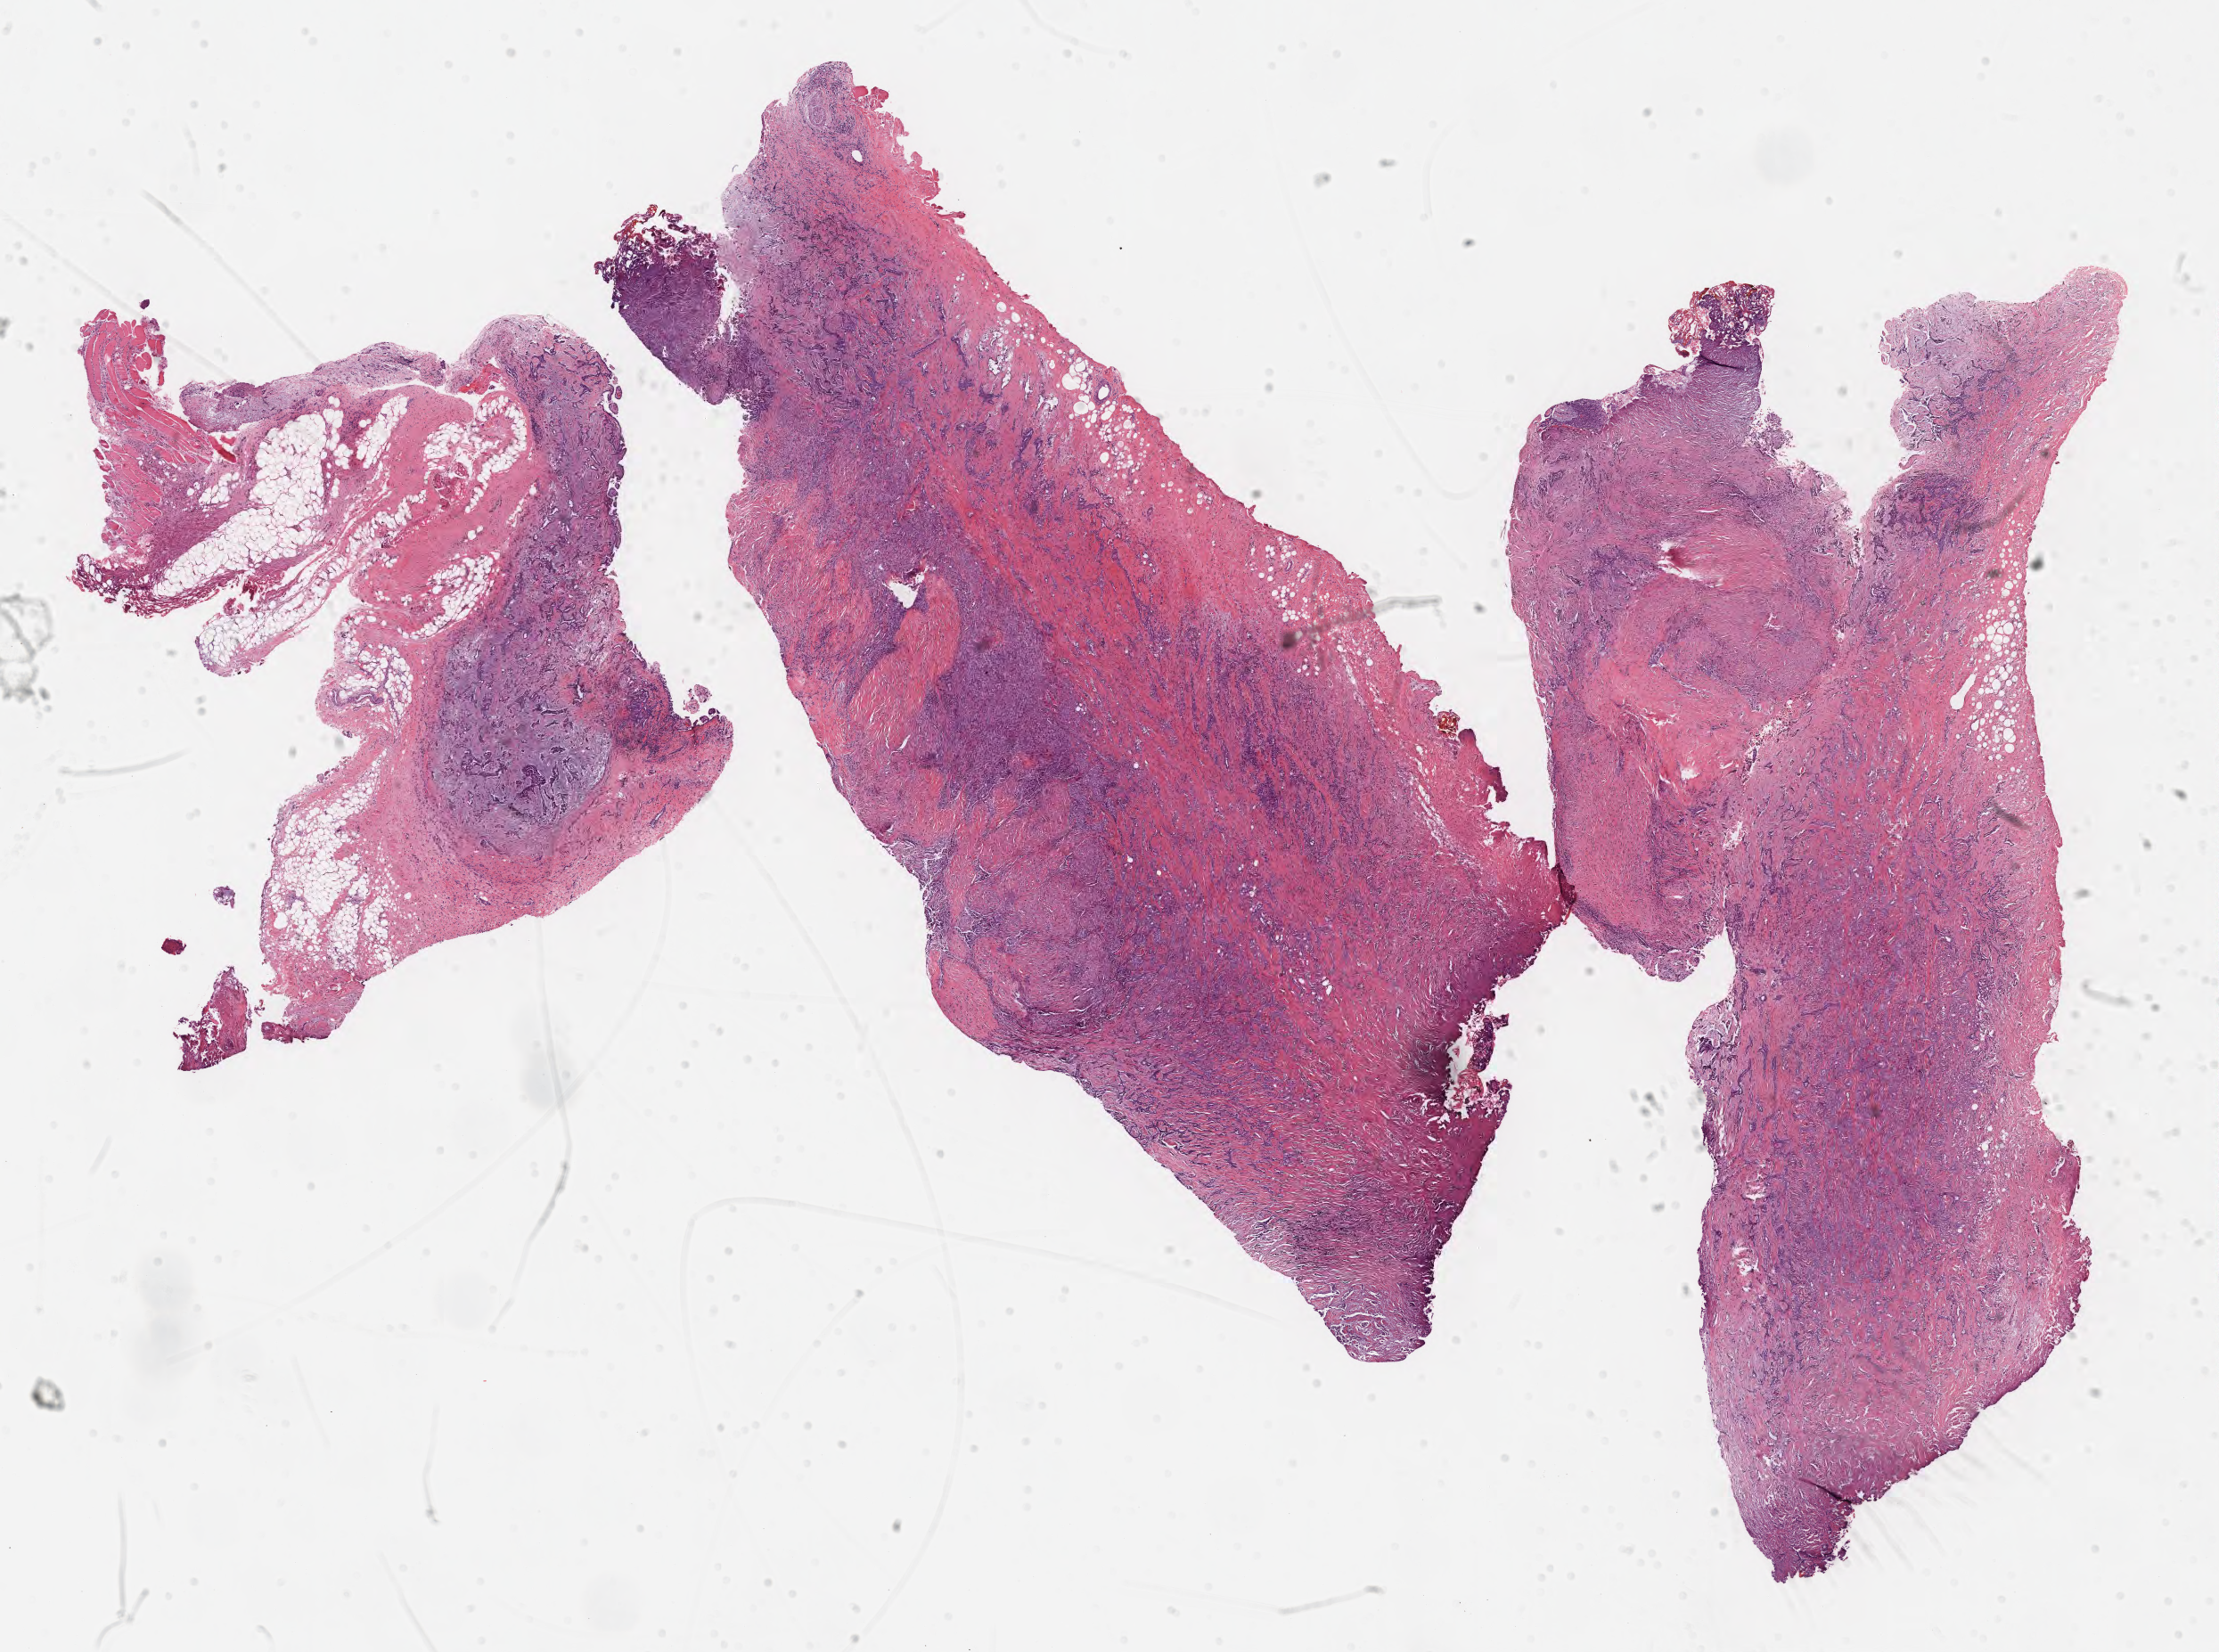
Digitized Hematoxylin and eosin (H&E) stained tissue section (whole slide), a low-resolution overview of the entire scanned area, about 20.1 x 15.0 mm; formalin-fixed paraffin-embedded (FFPE) diagnostic section; primary tumour sample from the mesothelium. Male patient; age at initial diagnosis 69 years.
Pathologic diagnosis: Epithelioid mesothelioma, malignant (pleura, NOS). AJCC pathologic stage: II (6th edition).